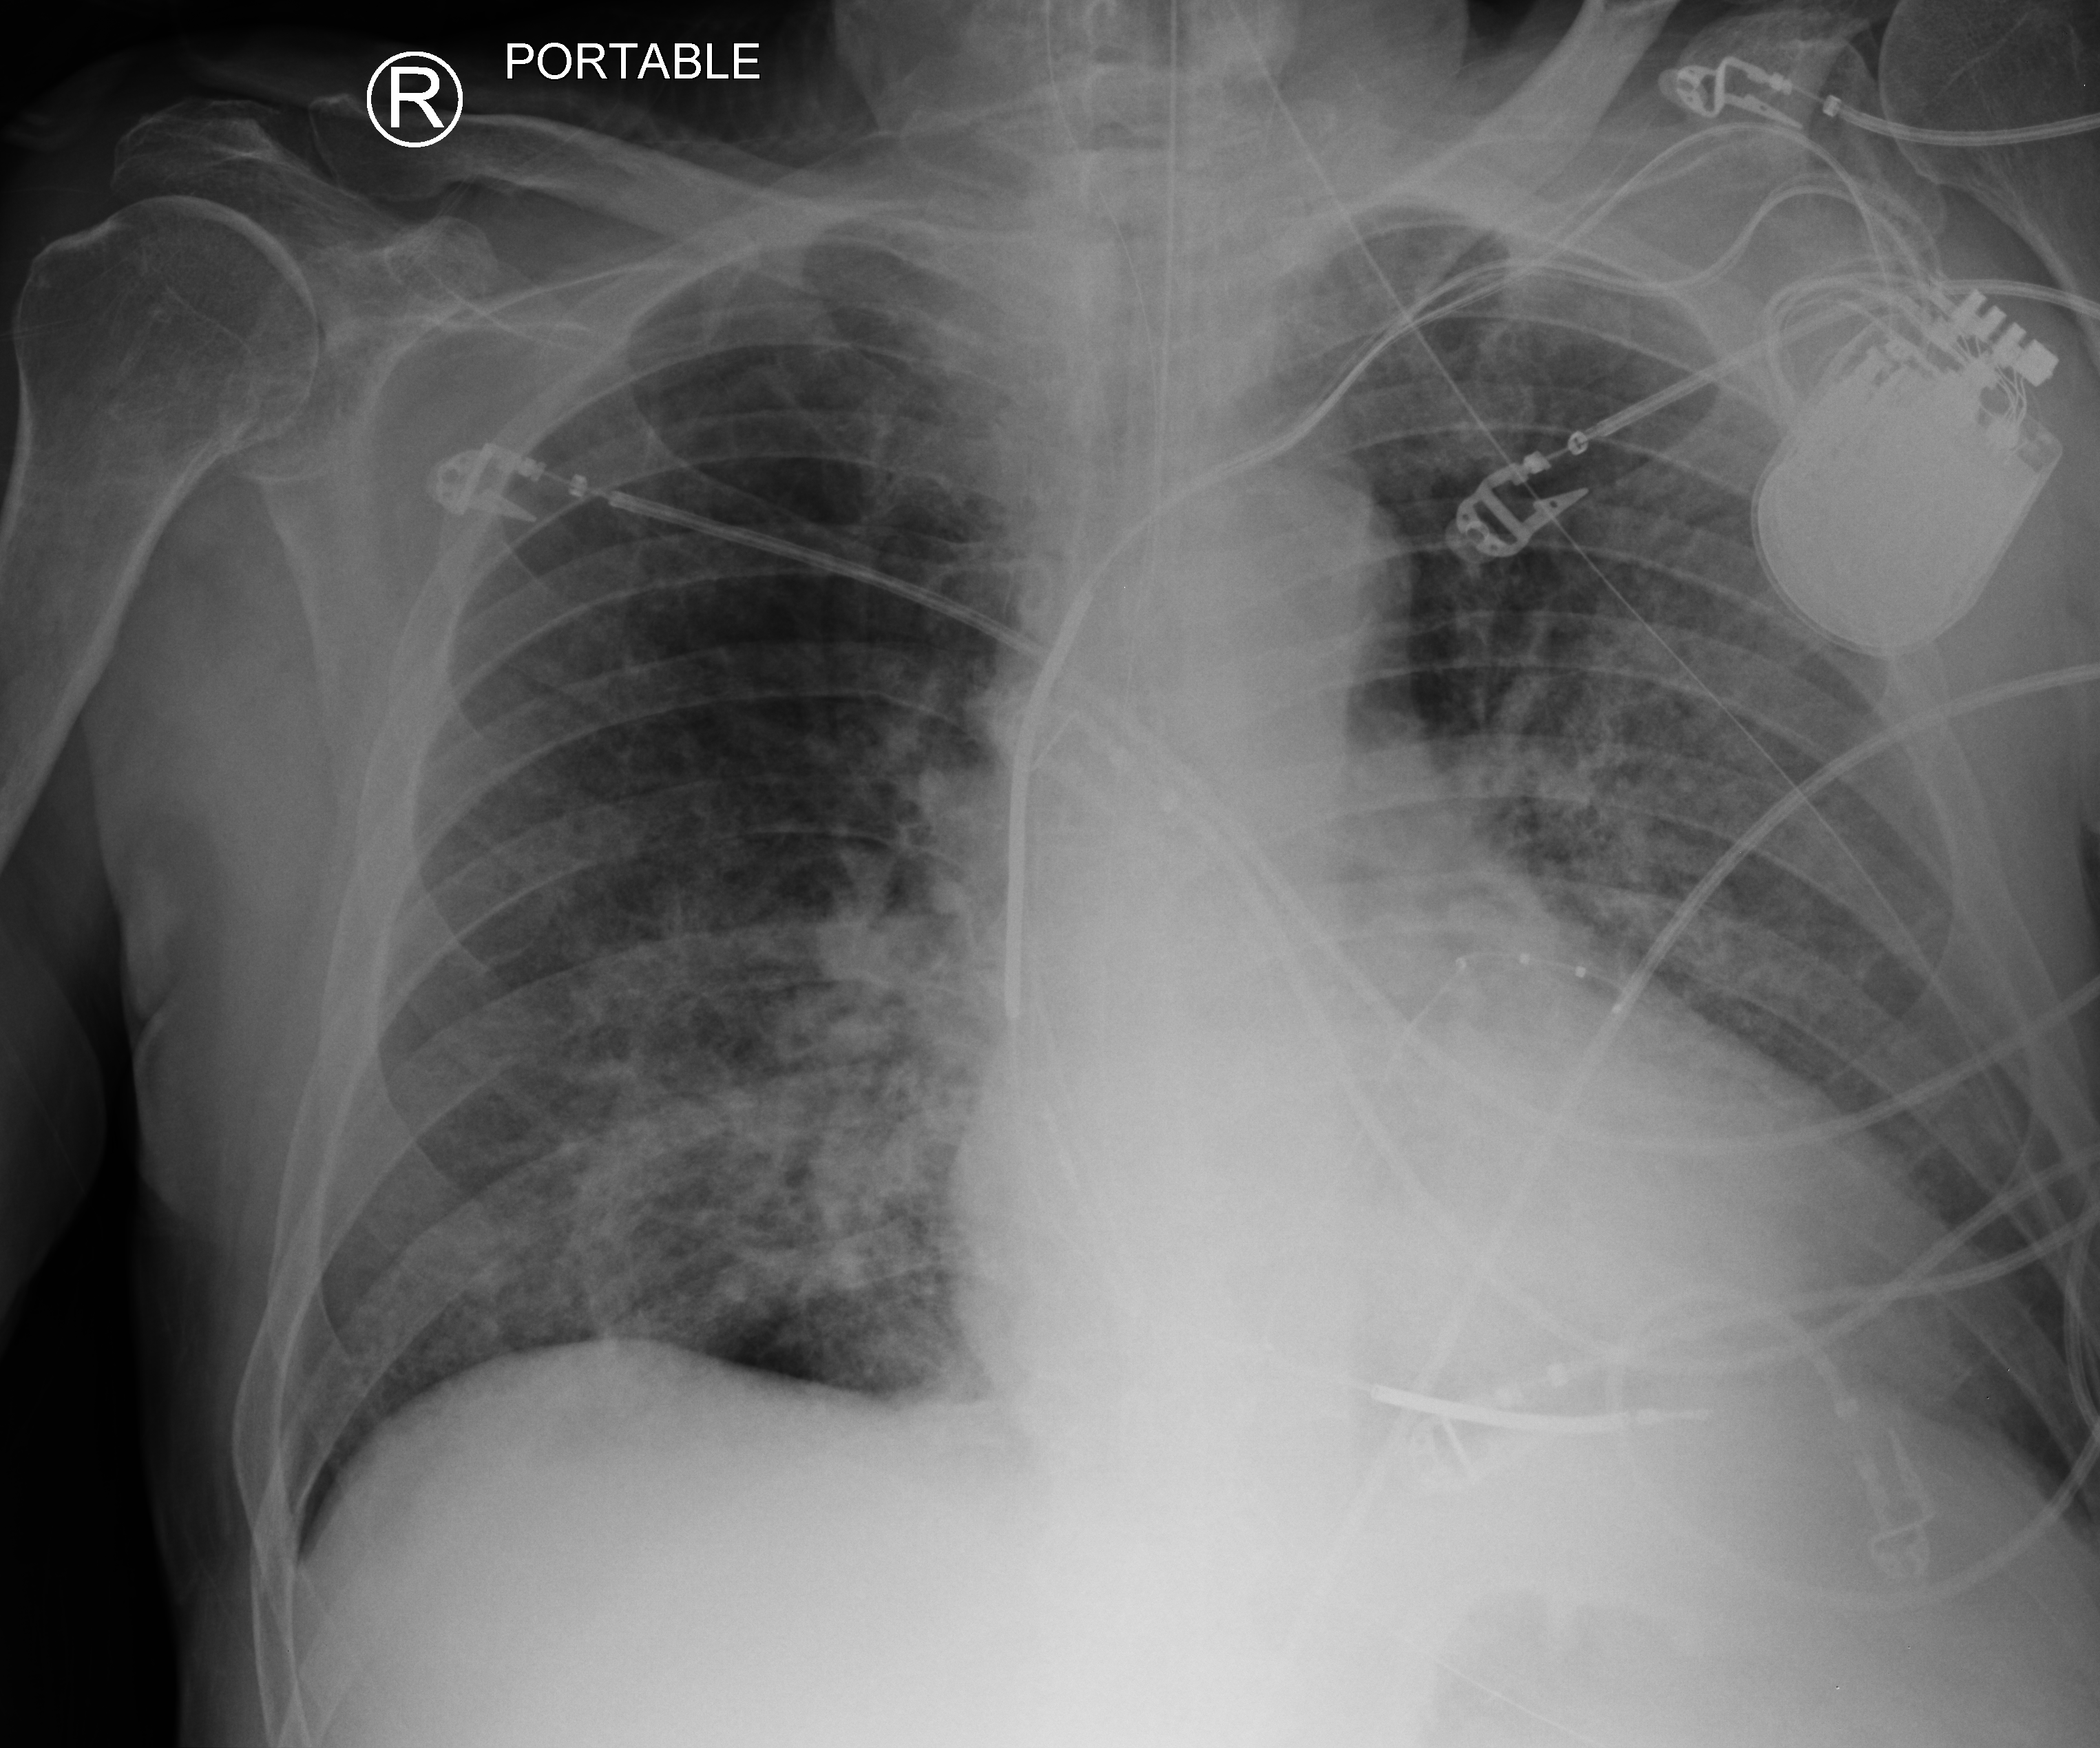
Portable chest radiograph. Patient hospitalised with COVID-19; male, aged 60–74 years.
From the hospital-stay record, not from the radiograph (when in the stay this image was taken is not recorded):
- admitted to intensive care during this hospital stay: yes
- diabetes (admission record): yes
- COPD (admission record): no